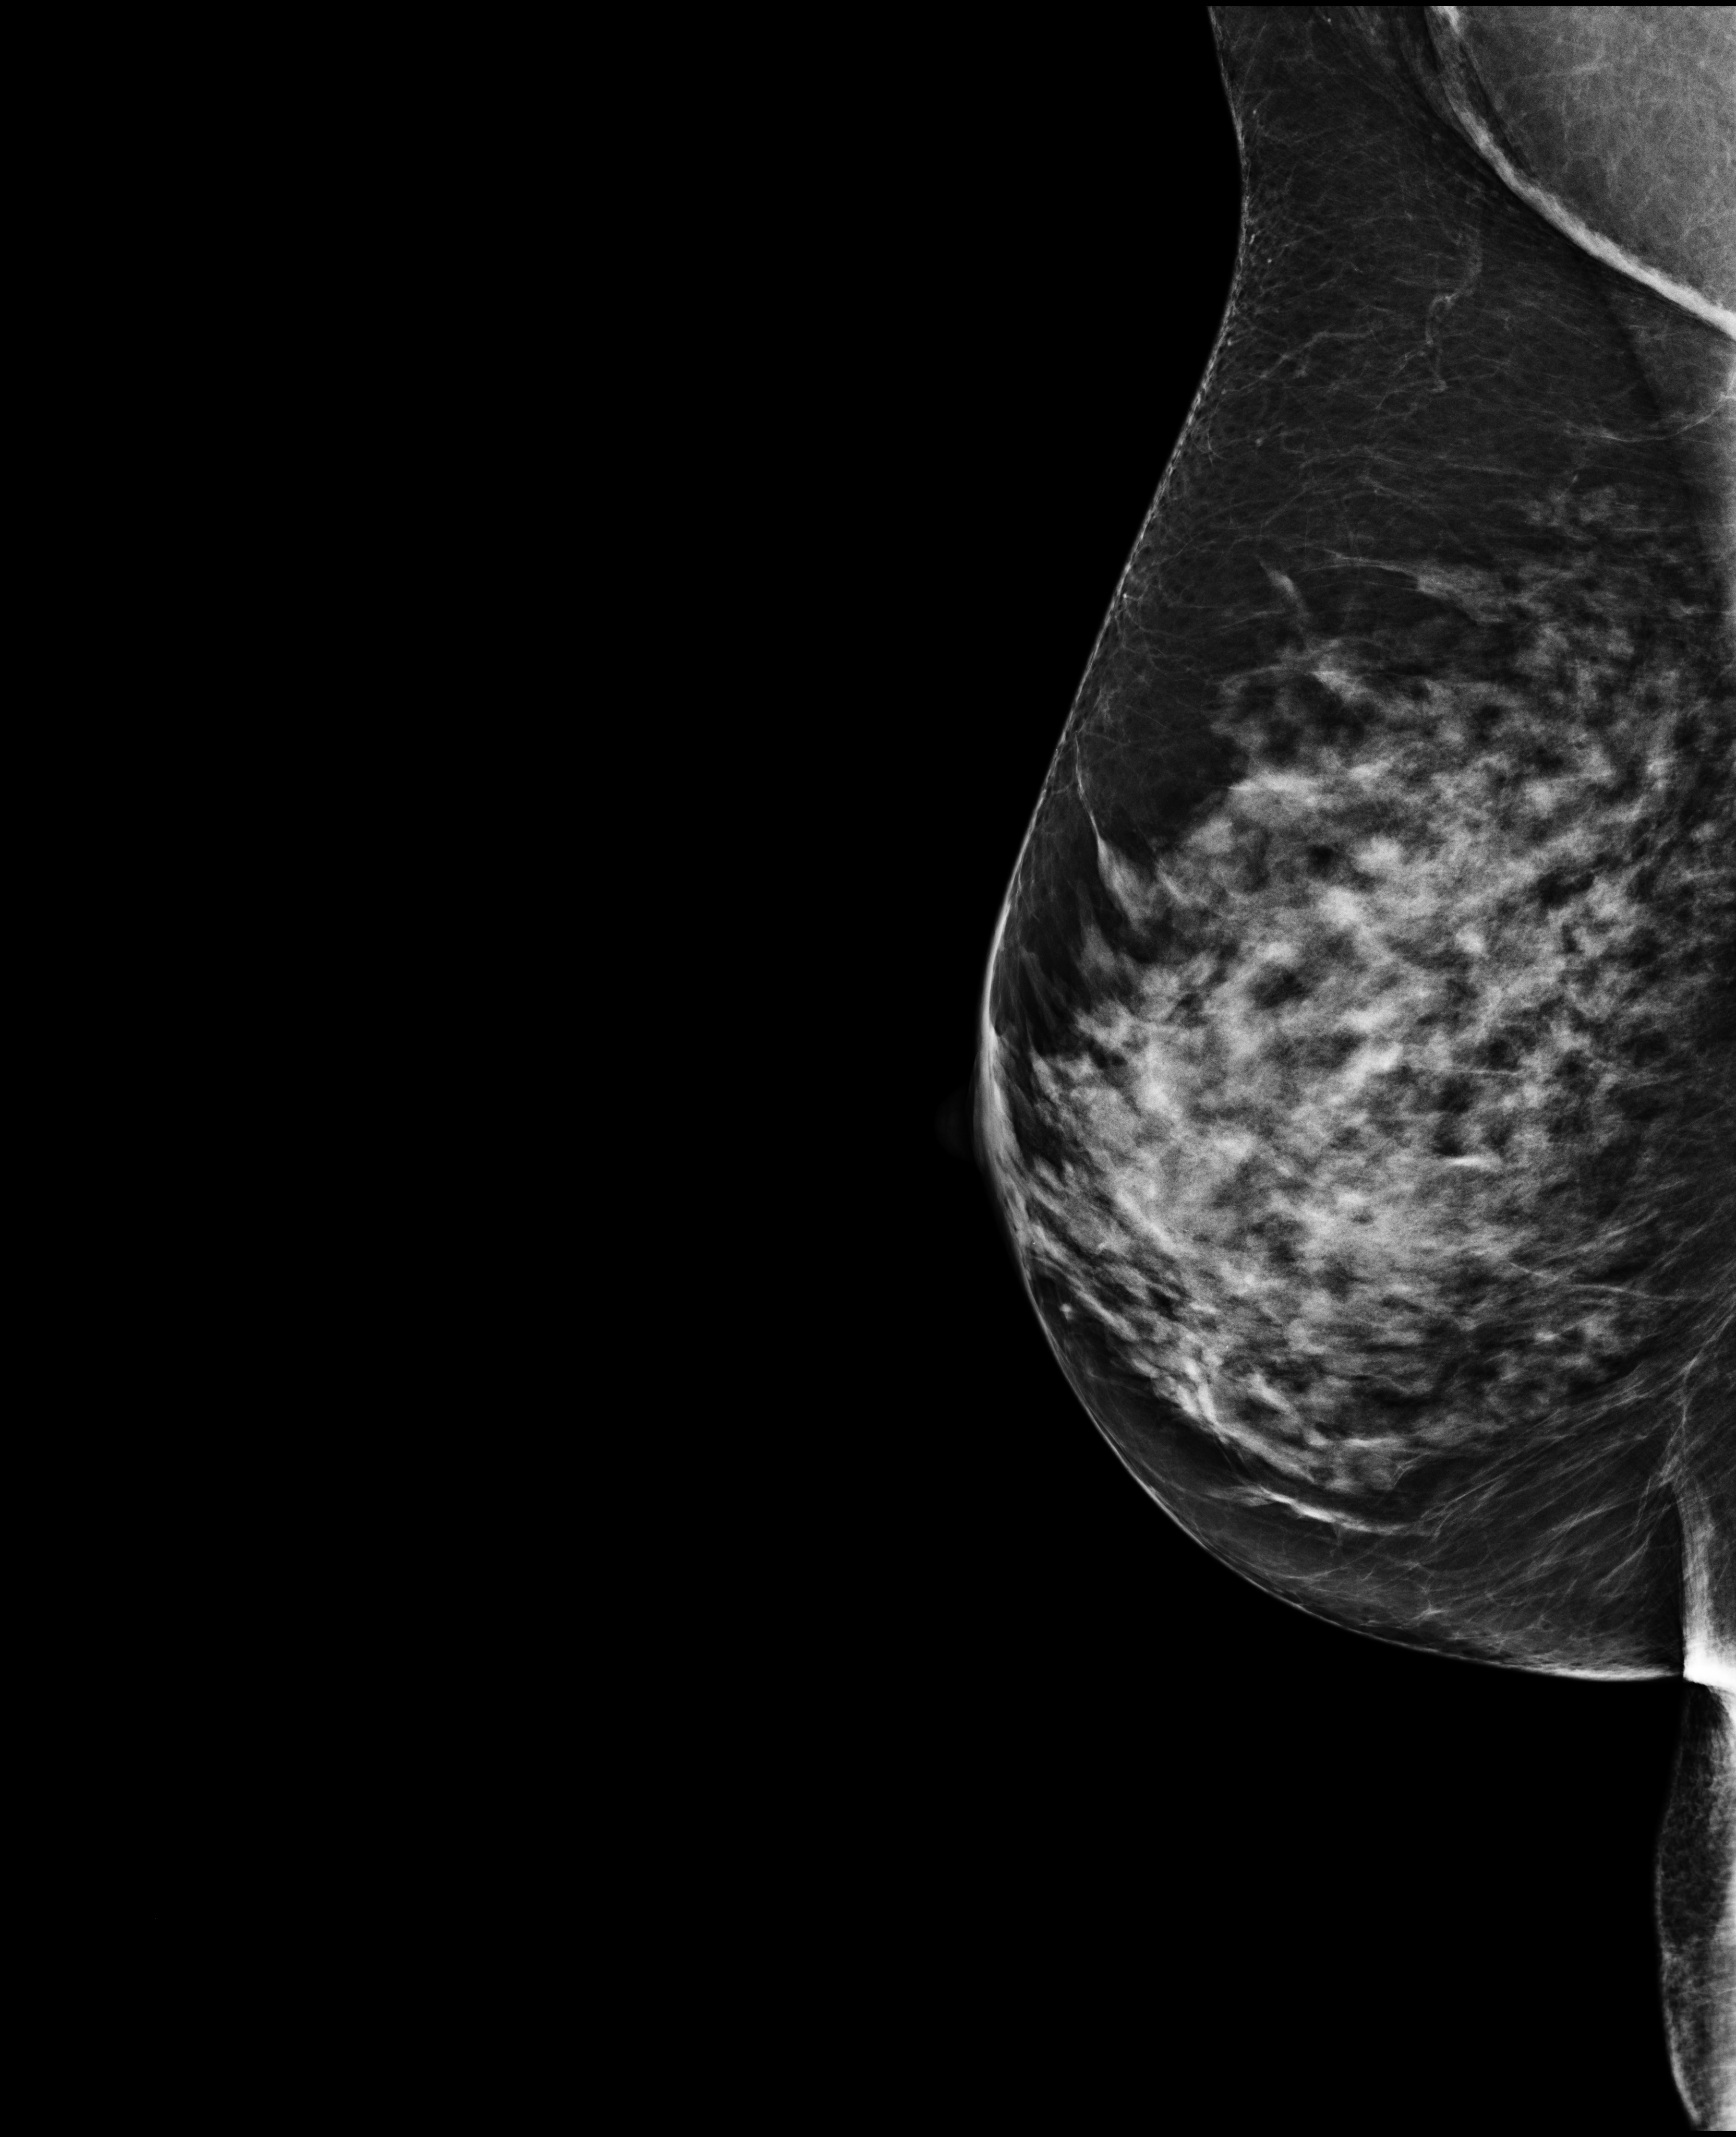
Digital mammogram (FFDM); right breast; medio-lateral oblique projection; screening examination; system: Selenia Dimensions. Patient aged 66 years (female).
BI-RADS breast density category at the screening exam (both breasts, scale 1–4): 3. Final BI-RADS category for the screening round (tomosynthesis exam, both breasts): category 1. Recall: no recall after this screen.